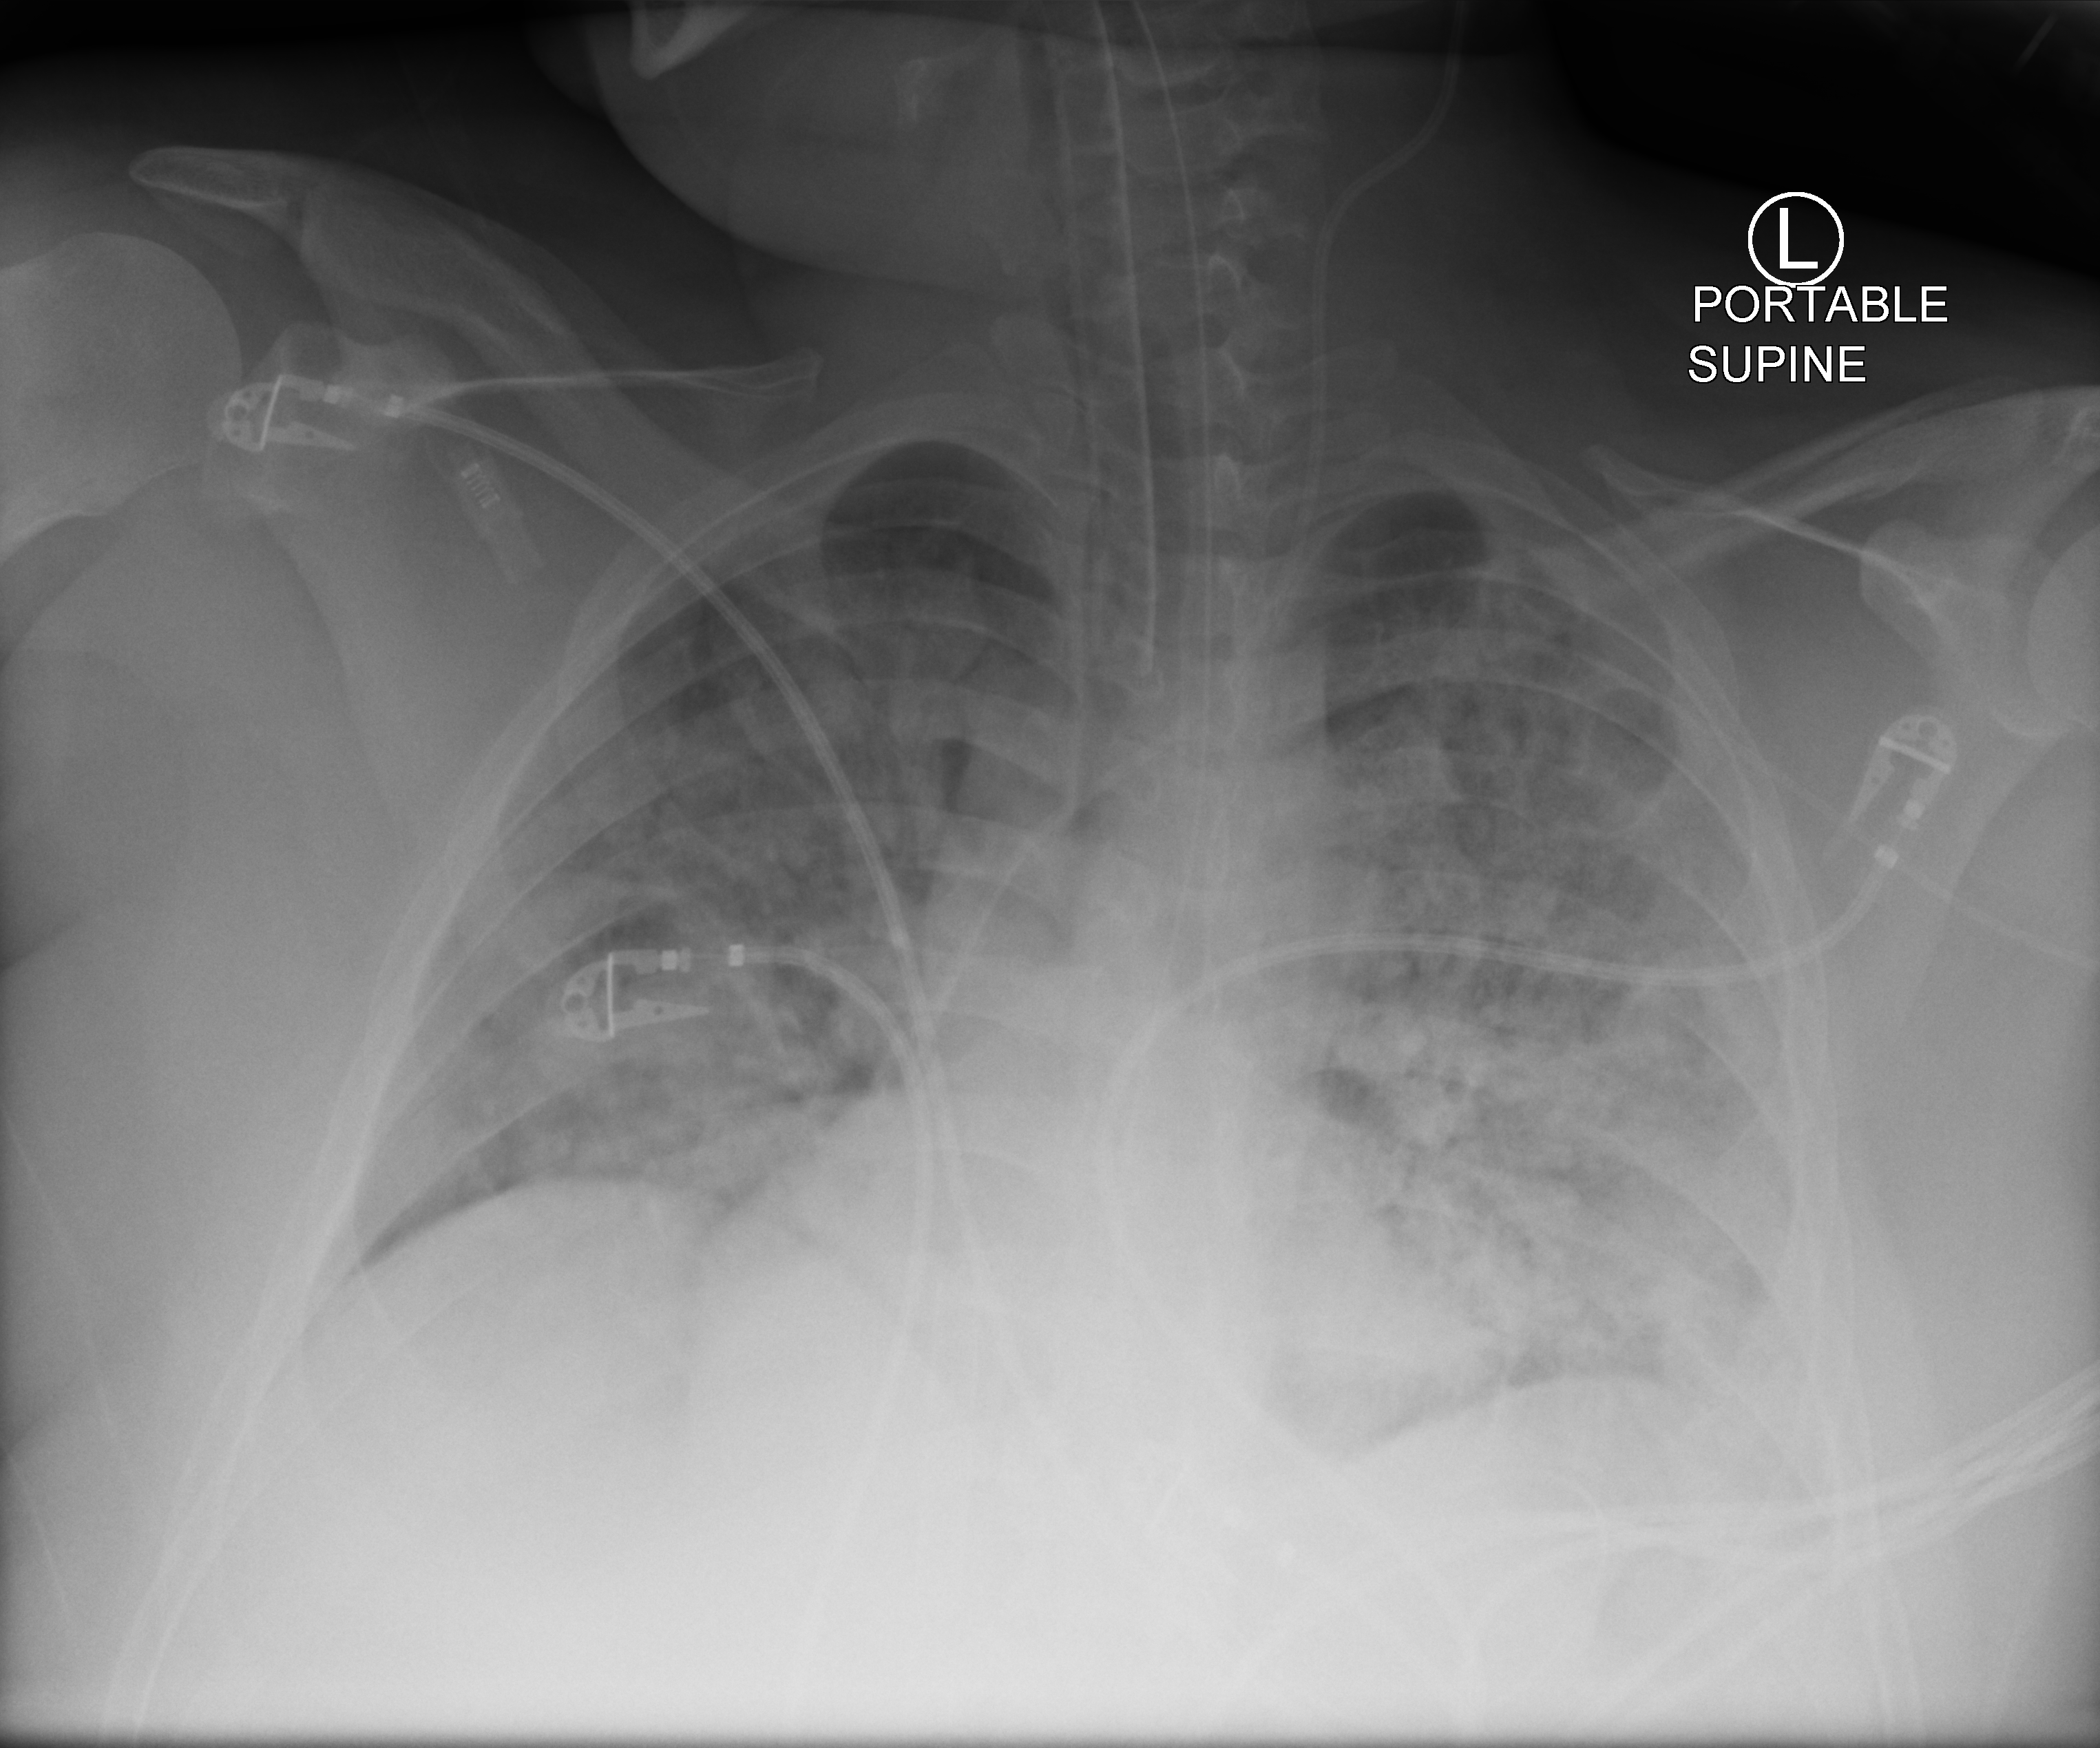
Bedside chest radiograph (computed radiography), anteroposterior (AP) projection. Patient hospitalised with COVID-19, aged 18–59 years.
From the hospital-stay record, not from the radiograph (when in the stay this image was taken is not recorded): length of hospital stay: 15 days; mechanically ventilated during this hospital stay: yes.